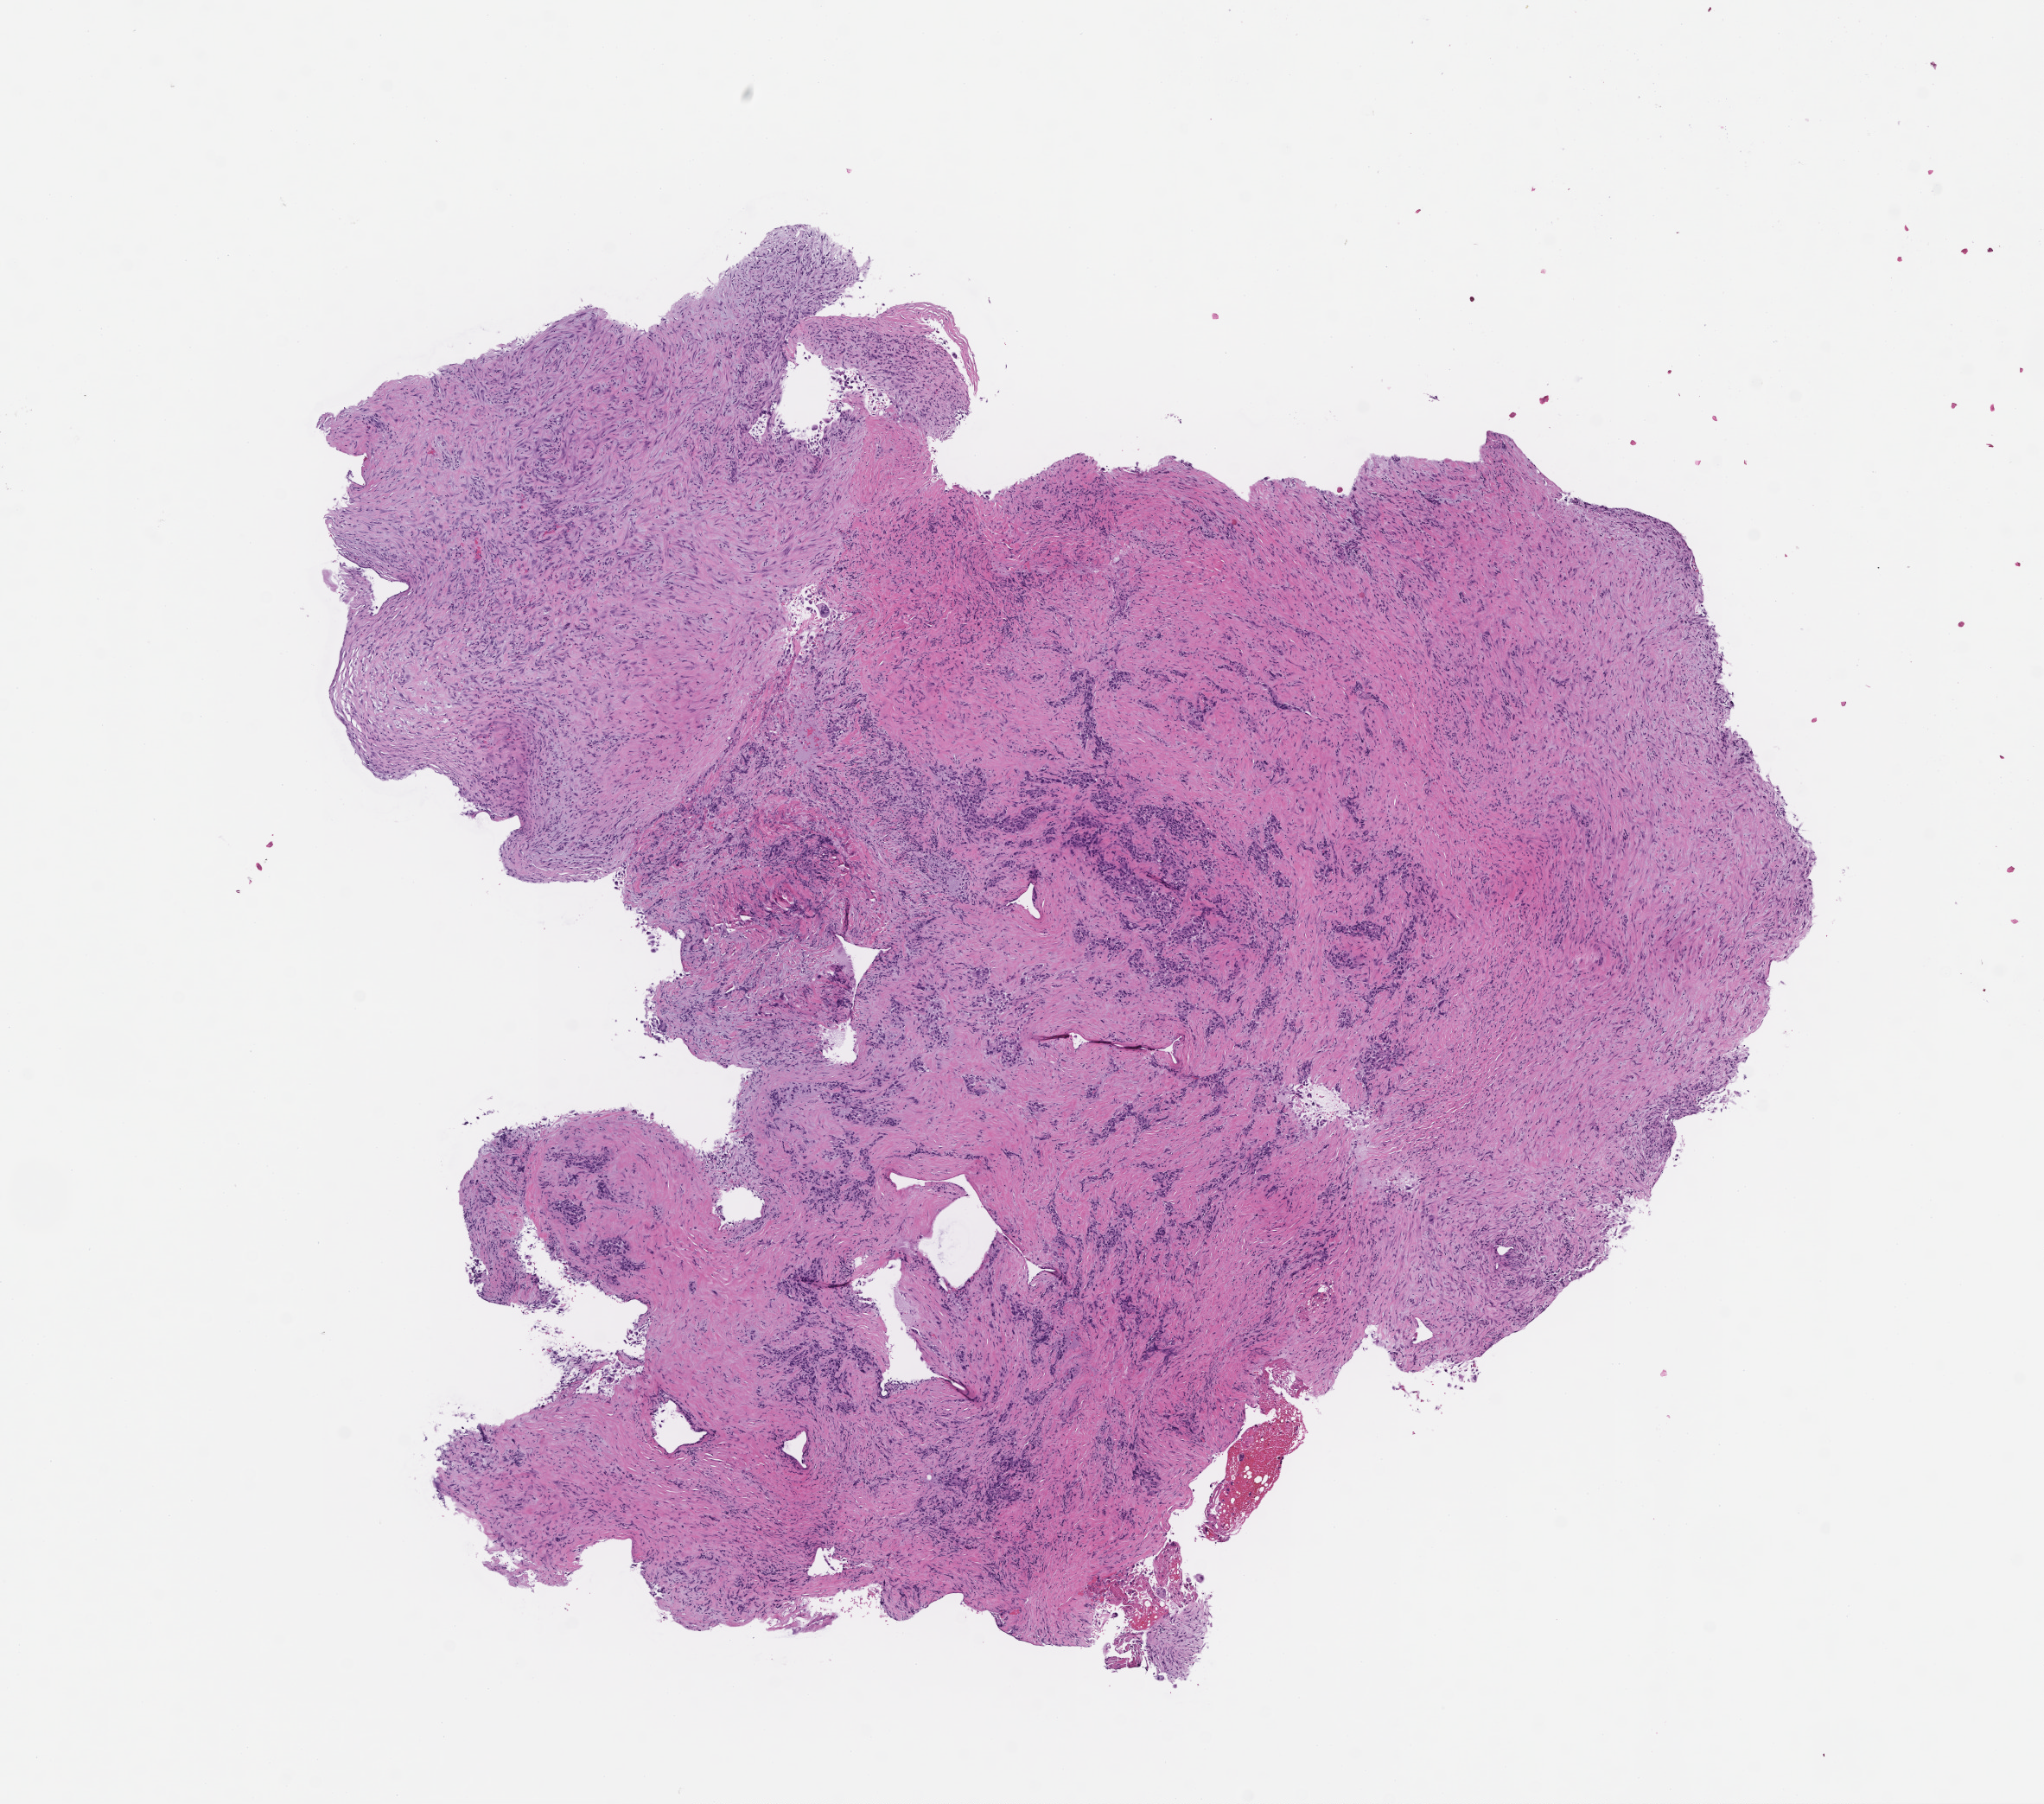
Whole-slide image, hematoxylin and eosin (H&E) stain — a low-resolution overview of the entire scanned area, about 9.5 x 8.4 mm. Formalin-fixed, paraffin-embedded (FFPE) tissue. Tissue site: lung. Specimen time point: collected at baseline (before treatment). Male patient.
This section: primary tumour tissue. Diagnosis: Non-Small Cell Lung Carcinoma.